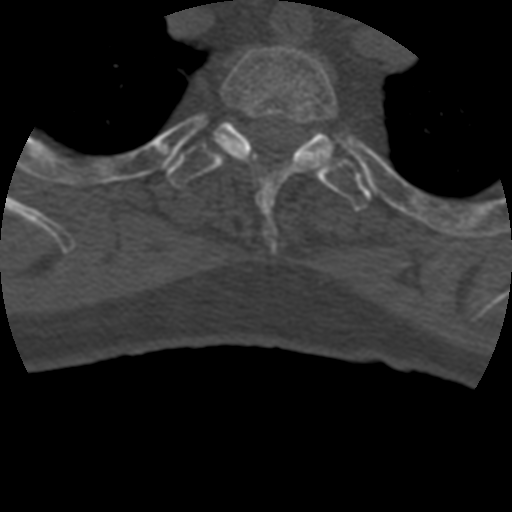
CT including the spine, one axial slice; position 361 of 399 along the scan axis; 120 kVp; bone window (W 1800 / L 400 HU); 512 × 512 image matrix, field of view 160 × 160 mm. Patient age 69 years. From the clinical record (not read from this slice): primary cancer: prostate.
Annotated regions visible in this slice (semi-automatically segmented with operator editing):
- T2 vertebra: box from (x=216, y=47) to (x=338, y=212) px
- T3 vertebra: (x=168, y=121)–(x=373, y=210)